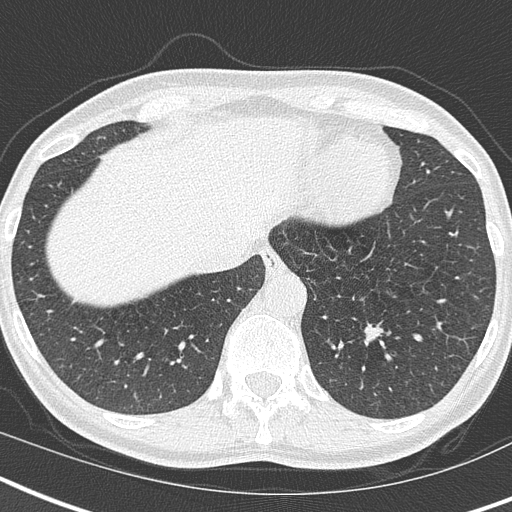
Low-dose screening chest CT, axial slice; third screening round (two years after baseline); lung window (W 1500 / L -600 HU); lung (sharp) reconstruction kernel (B50f); 120 kVp; slice 127 of 173 in the series. Female, age 55 years at enrolment. Current smoker at enrolment.
Expert reader's lesion annotation, bounding box [x1, y1, x2, y2] px = [348, 308, 399, 361]. The screening reader recorded 2 non-calcified nodules or masses ≥4 mm on this exam (left lower lobe, right upper lobe); which of them this box marks is not recorded. Lung cancer was diagnosed 349 days after this screen: adenocarcinoma, NOS, left lower lobe, well differentiated (G1), stage IA (AJCC 6th edition), 11 mm at pathology.